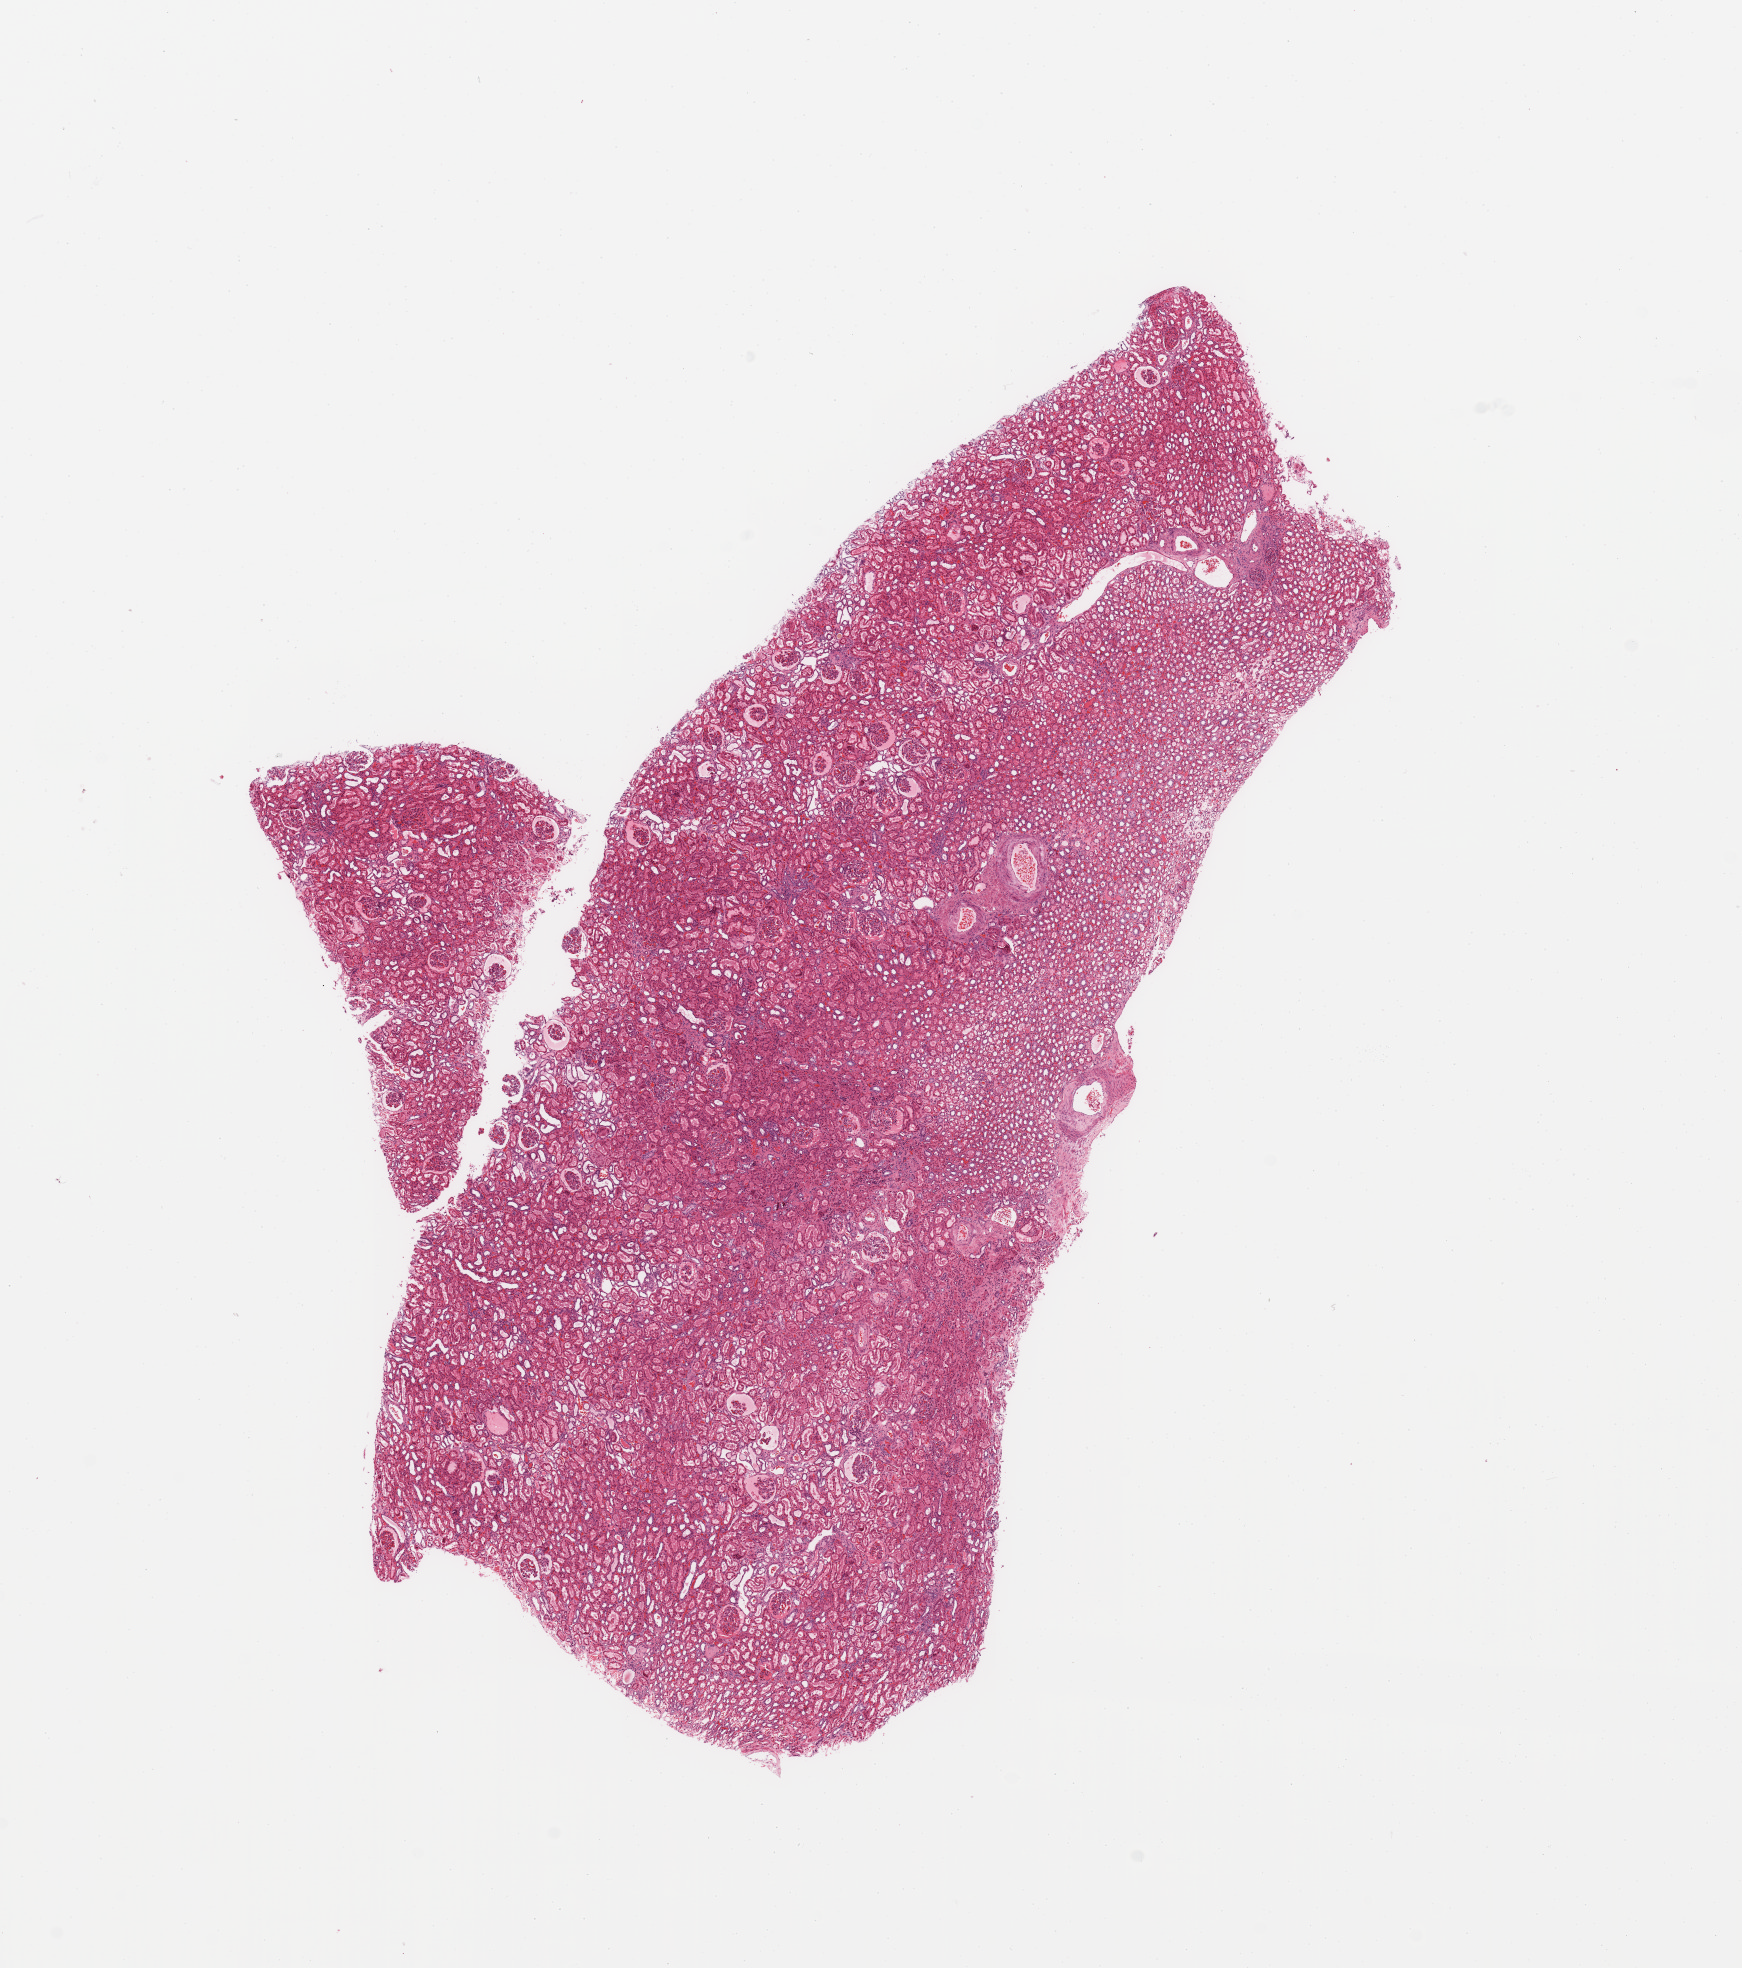
Whole-slide histology image, Hematoxylin and eosin (H&E) stained, shown as a low-resolution overview of the whole scanned area (about 13.8 x 15.6 mm). Normal (non-tumour) tissue sample, sampled site: kidney. Patient: male, age 52 years.
* this section: normal (non-tumour) tissue from the same patient
* patient diagnosis: Renal cell carcinoma, NOS